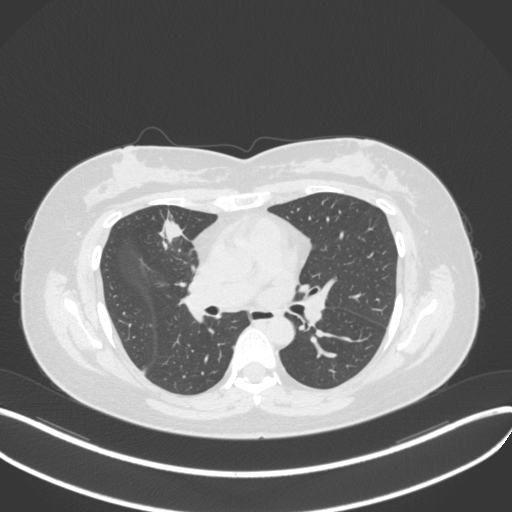
Chest CT, one axial slice; position 174 of 272 along the scan axis; reconstruction kernel B31f; lung window (W 1500 / L -600 HU); 1 mm slice thickness; 512 × 512 image matrix. Female patient, age 42 years. From the clinical record (not read from this slice): clinical TNM (as recorded): T1b N0 M0.
Annotated regions visible in this slice (bounding box drawn by a radiologist):
- lung tumour (recorded histology: adenocarcinoma): bounding box <154,211,188,252> (left, top, right, bottom; pixels)